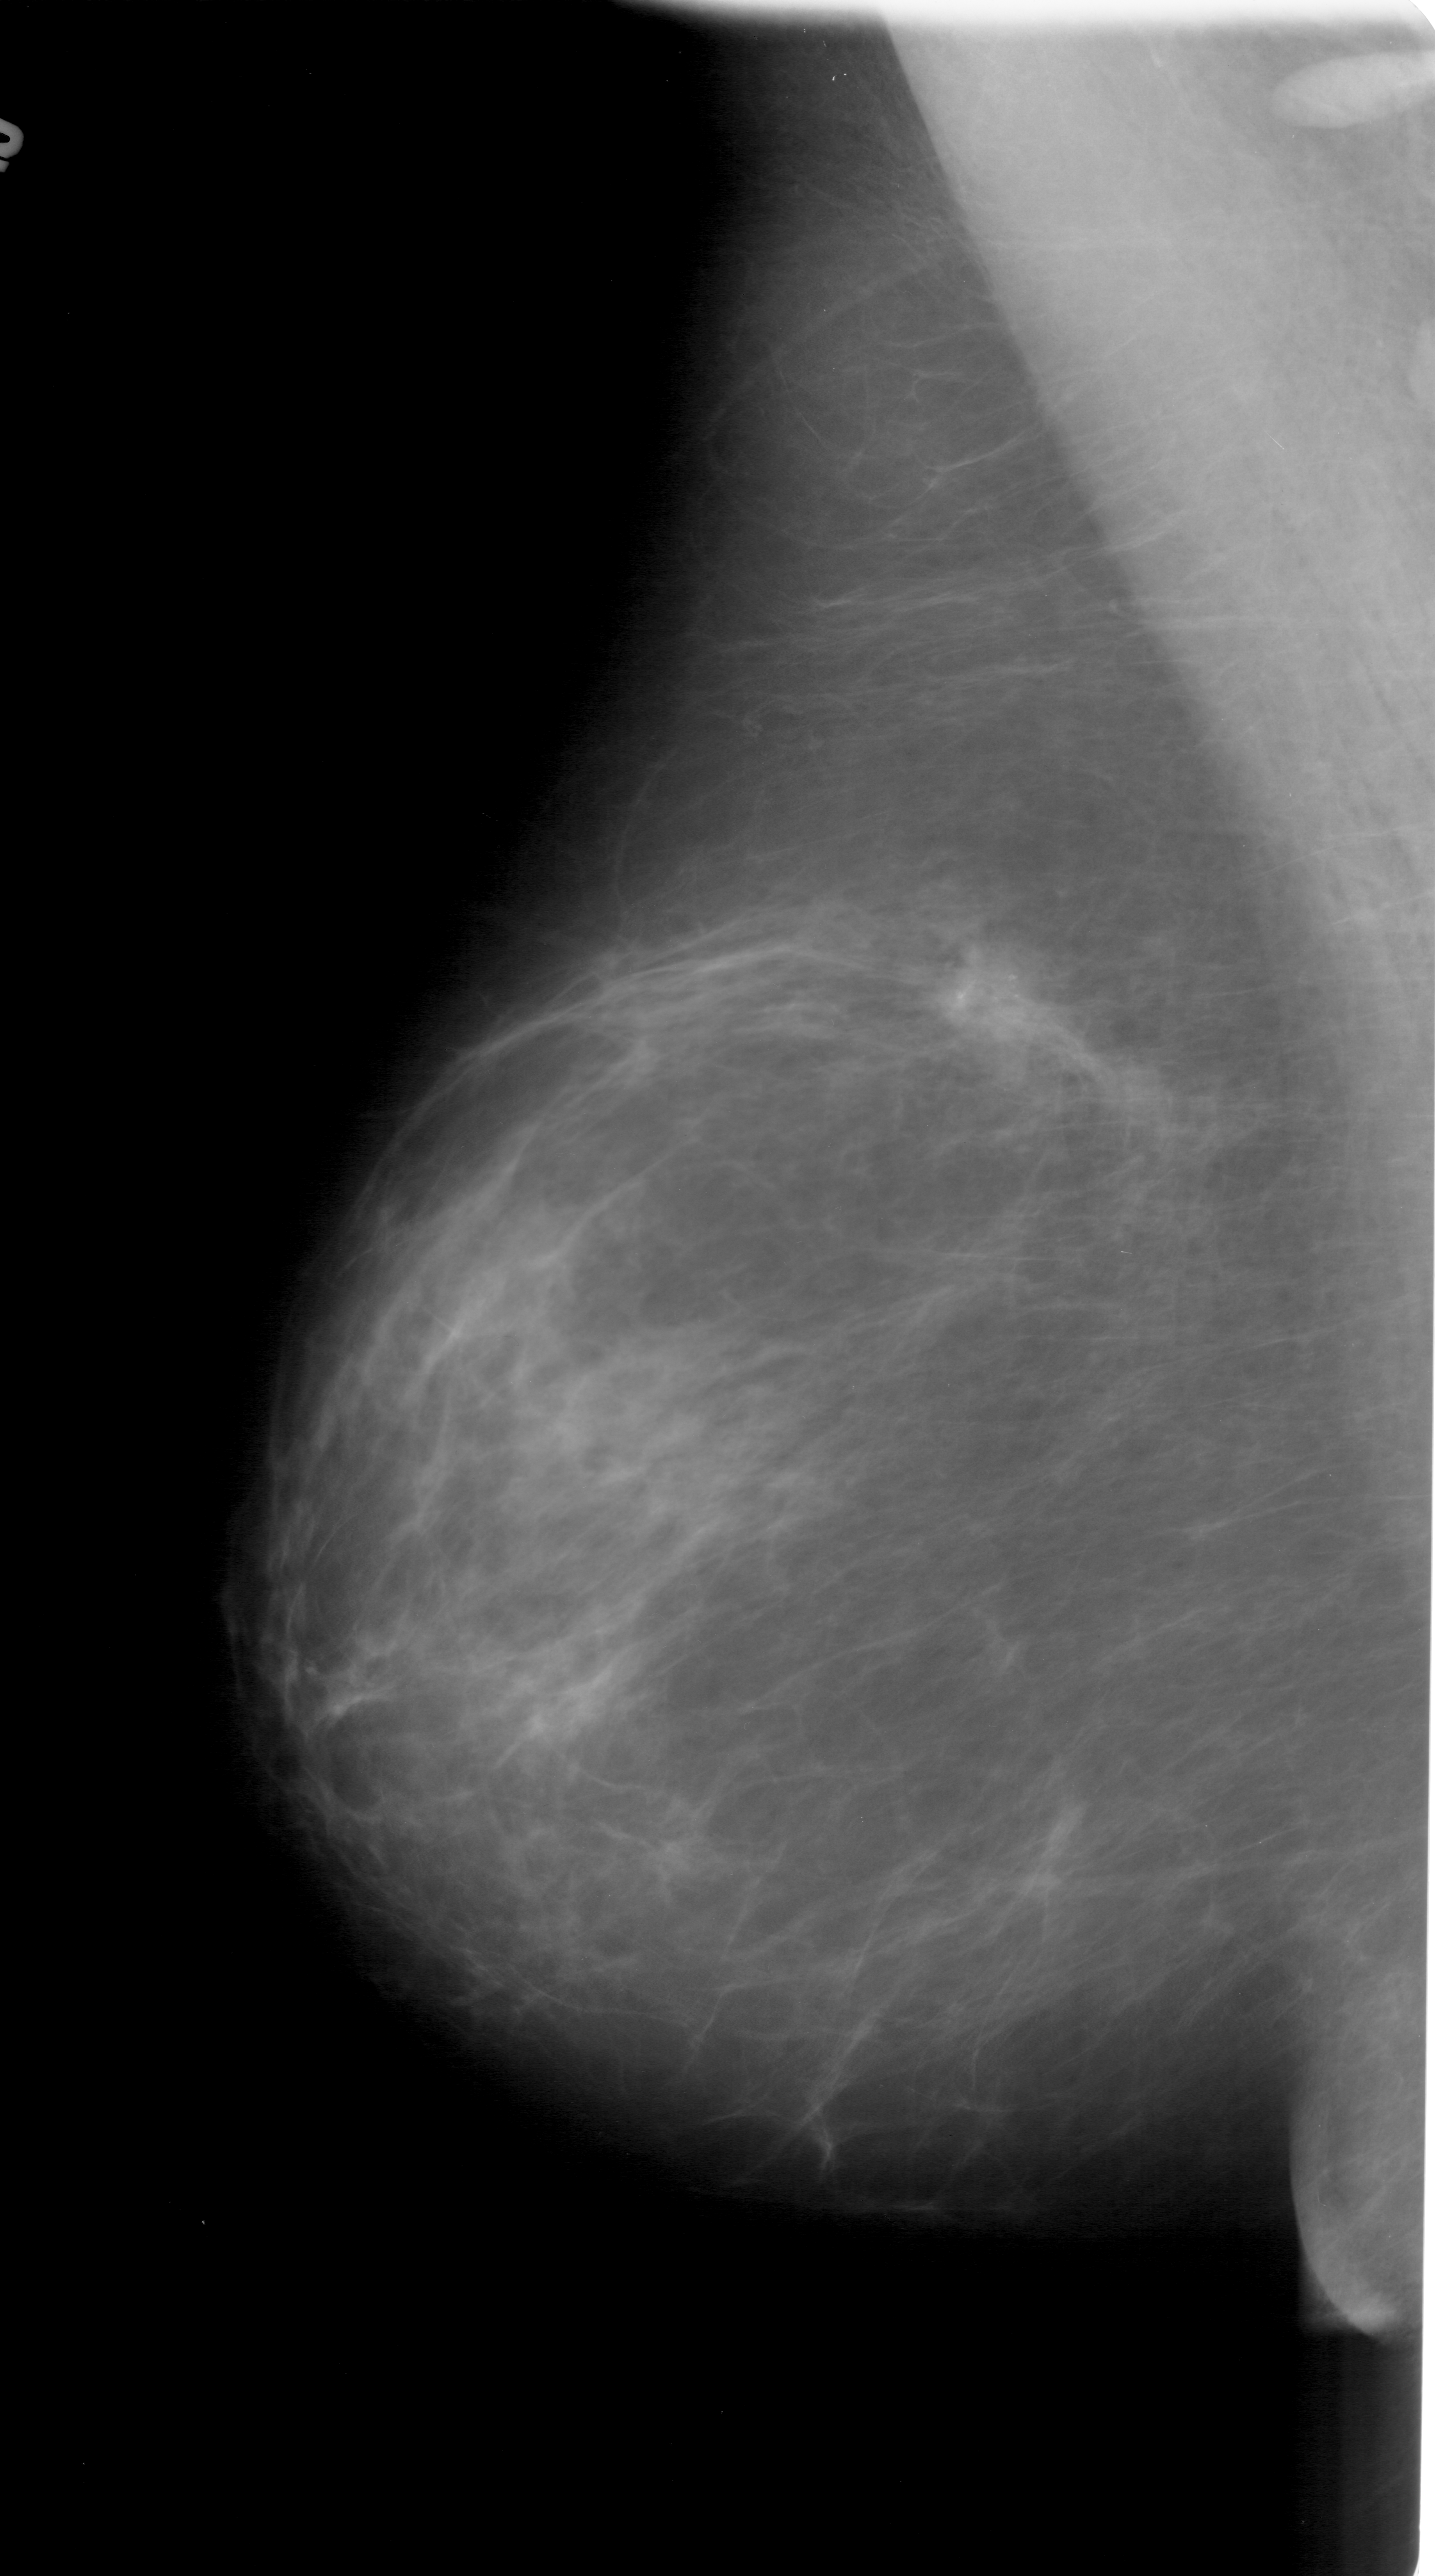
Digitized screen-film mammogram; left breast; MLO view; 1435 × 2576 image matrix.
Expert-marked regions of interest on this film, with their recorded descriptors:
- mass, shape asymmetric breast tissue, margins ill defined; BI-RADS assessment category 4; pathology result (as recorded, not read from the image): malignant: box from (x=911, y=940) to (x=1077, y=1069) px